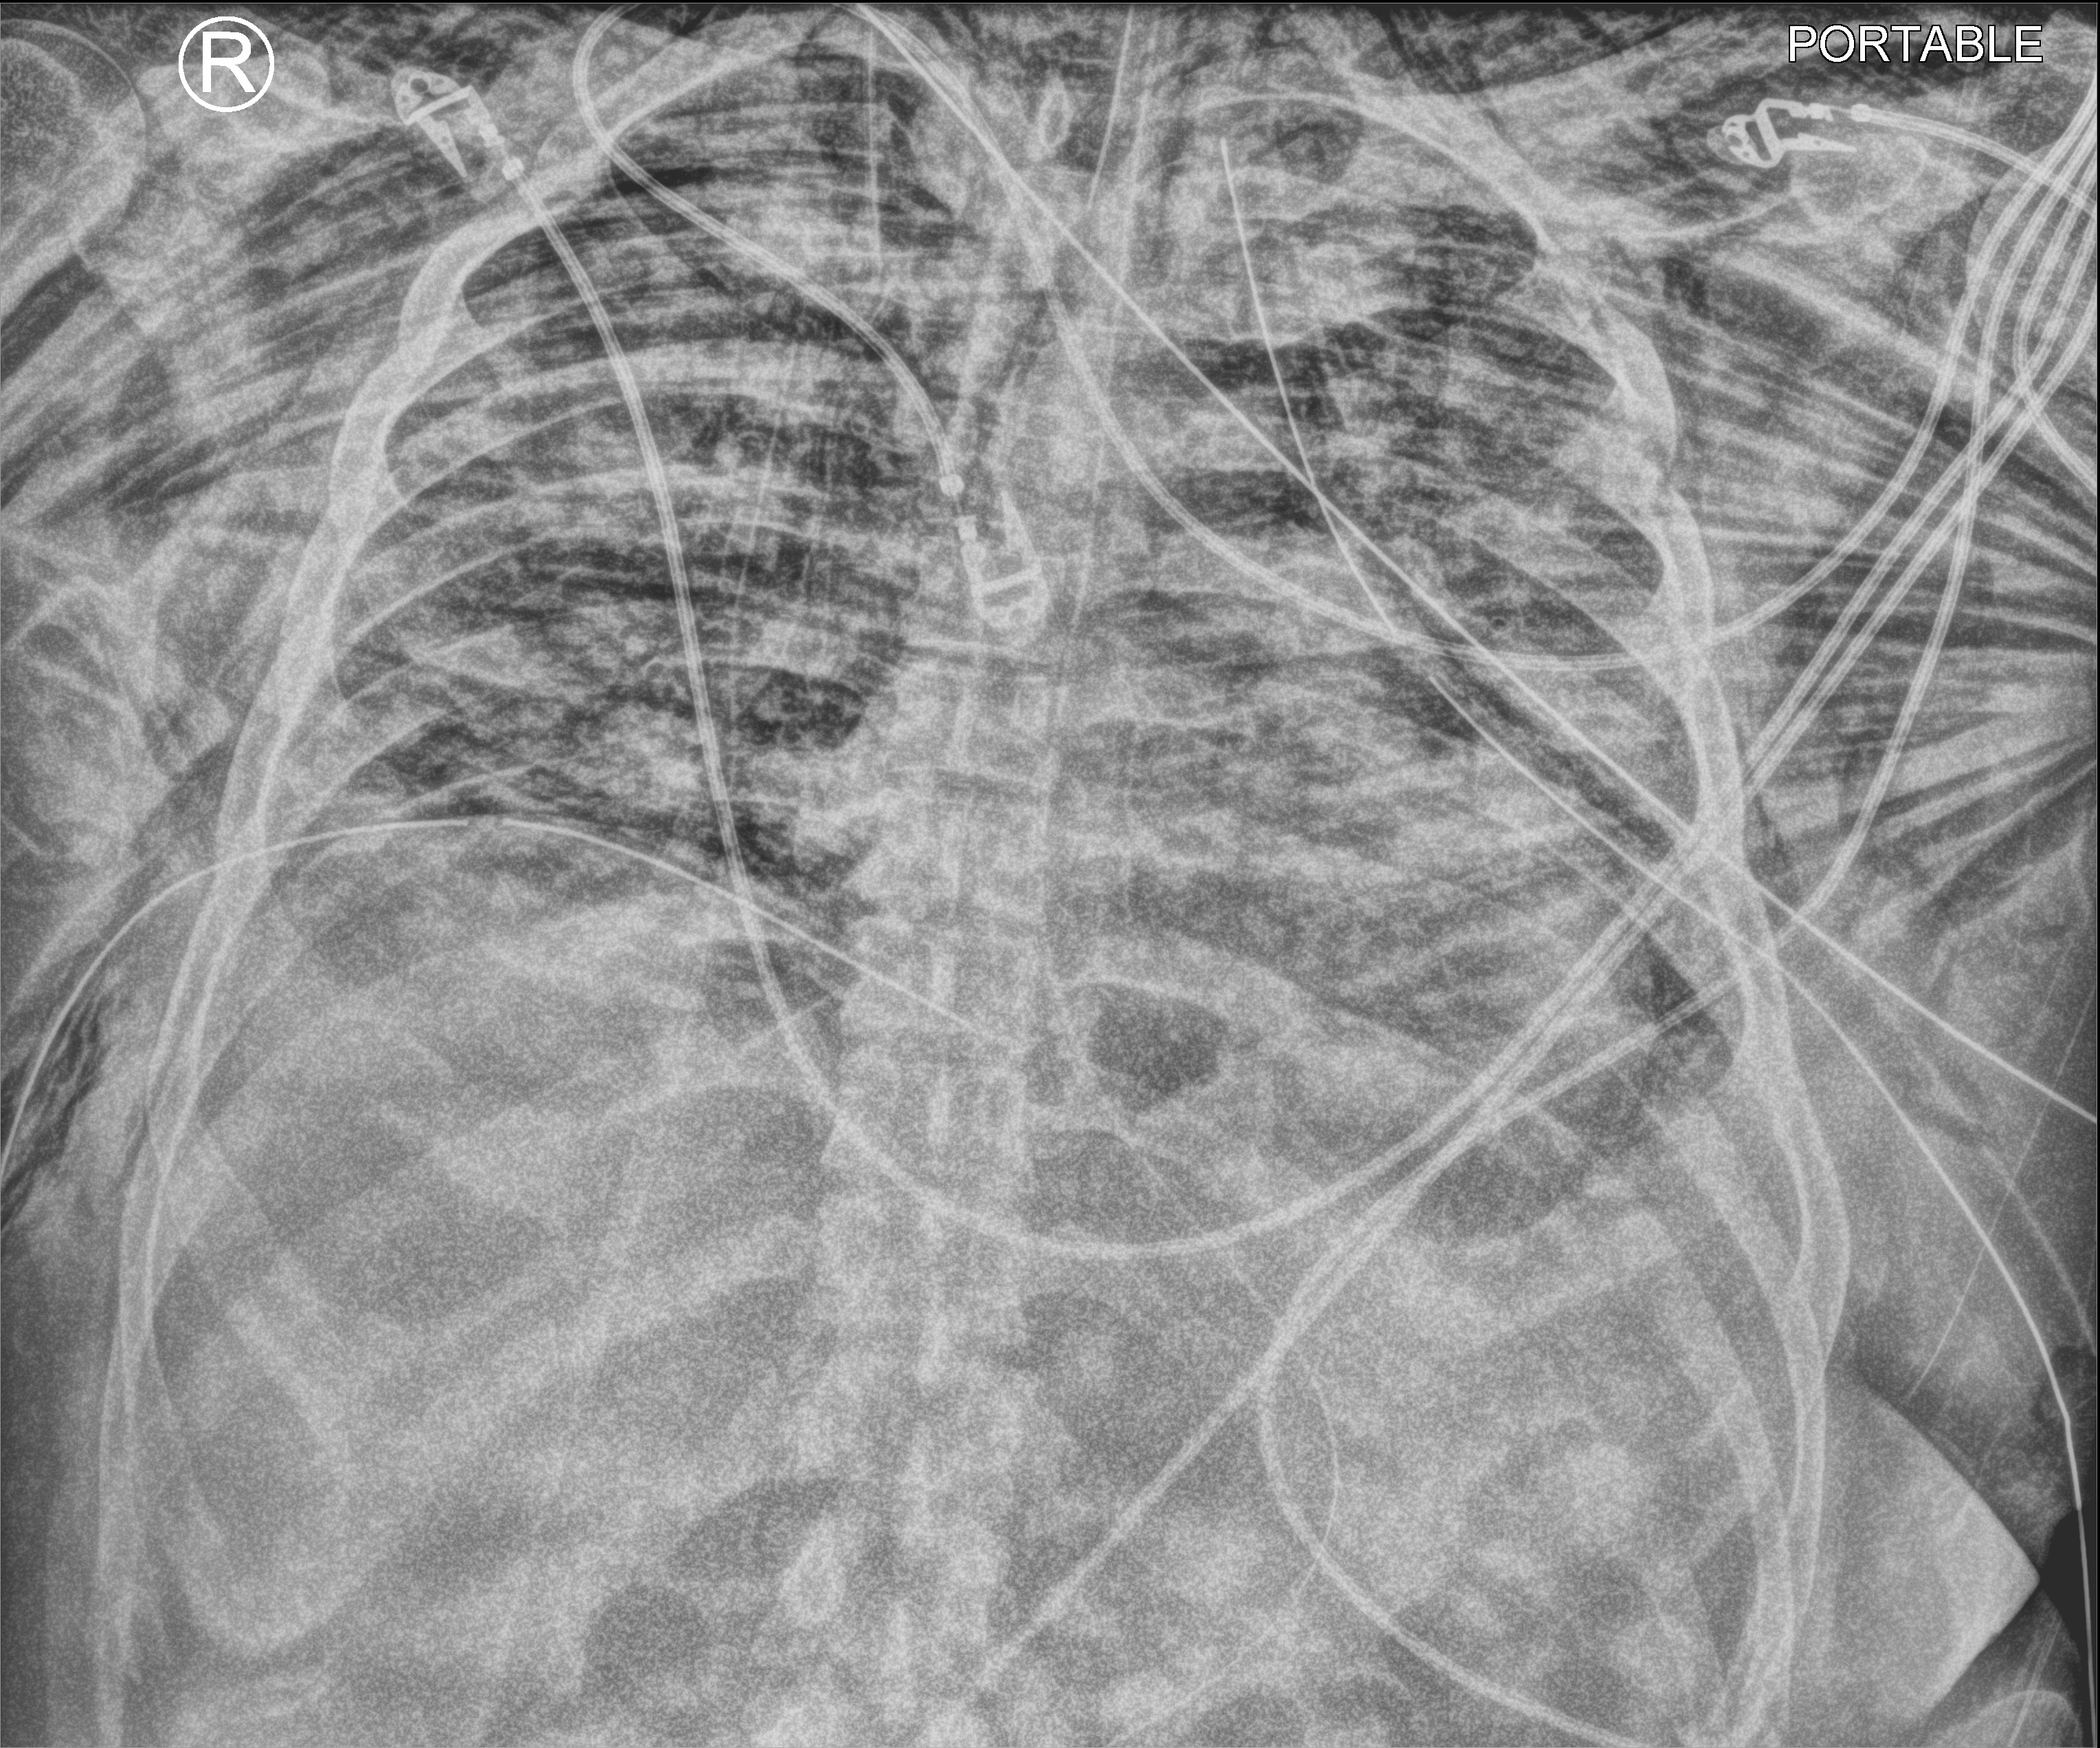
Bedside chest radiograph (computed radiography); anteroposterior (AP) projection. Patient hospitalised with COVID-19; male, aged 18–59 years.
Hospital-stay facts (about this admission, not read from this image; timing relative to this image not recorded): length of hospital stay: 29 days; mechanically ventilated during this hospital stay: yes; admitted to intensive care during this hospital stay: yes.